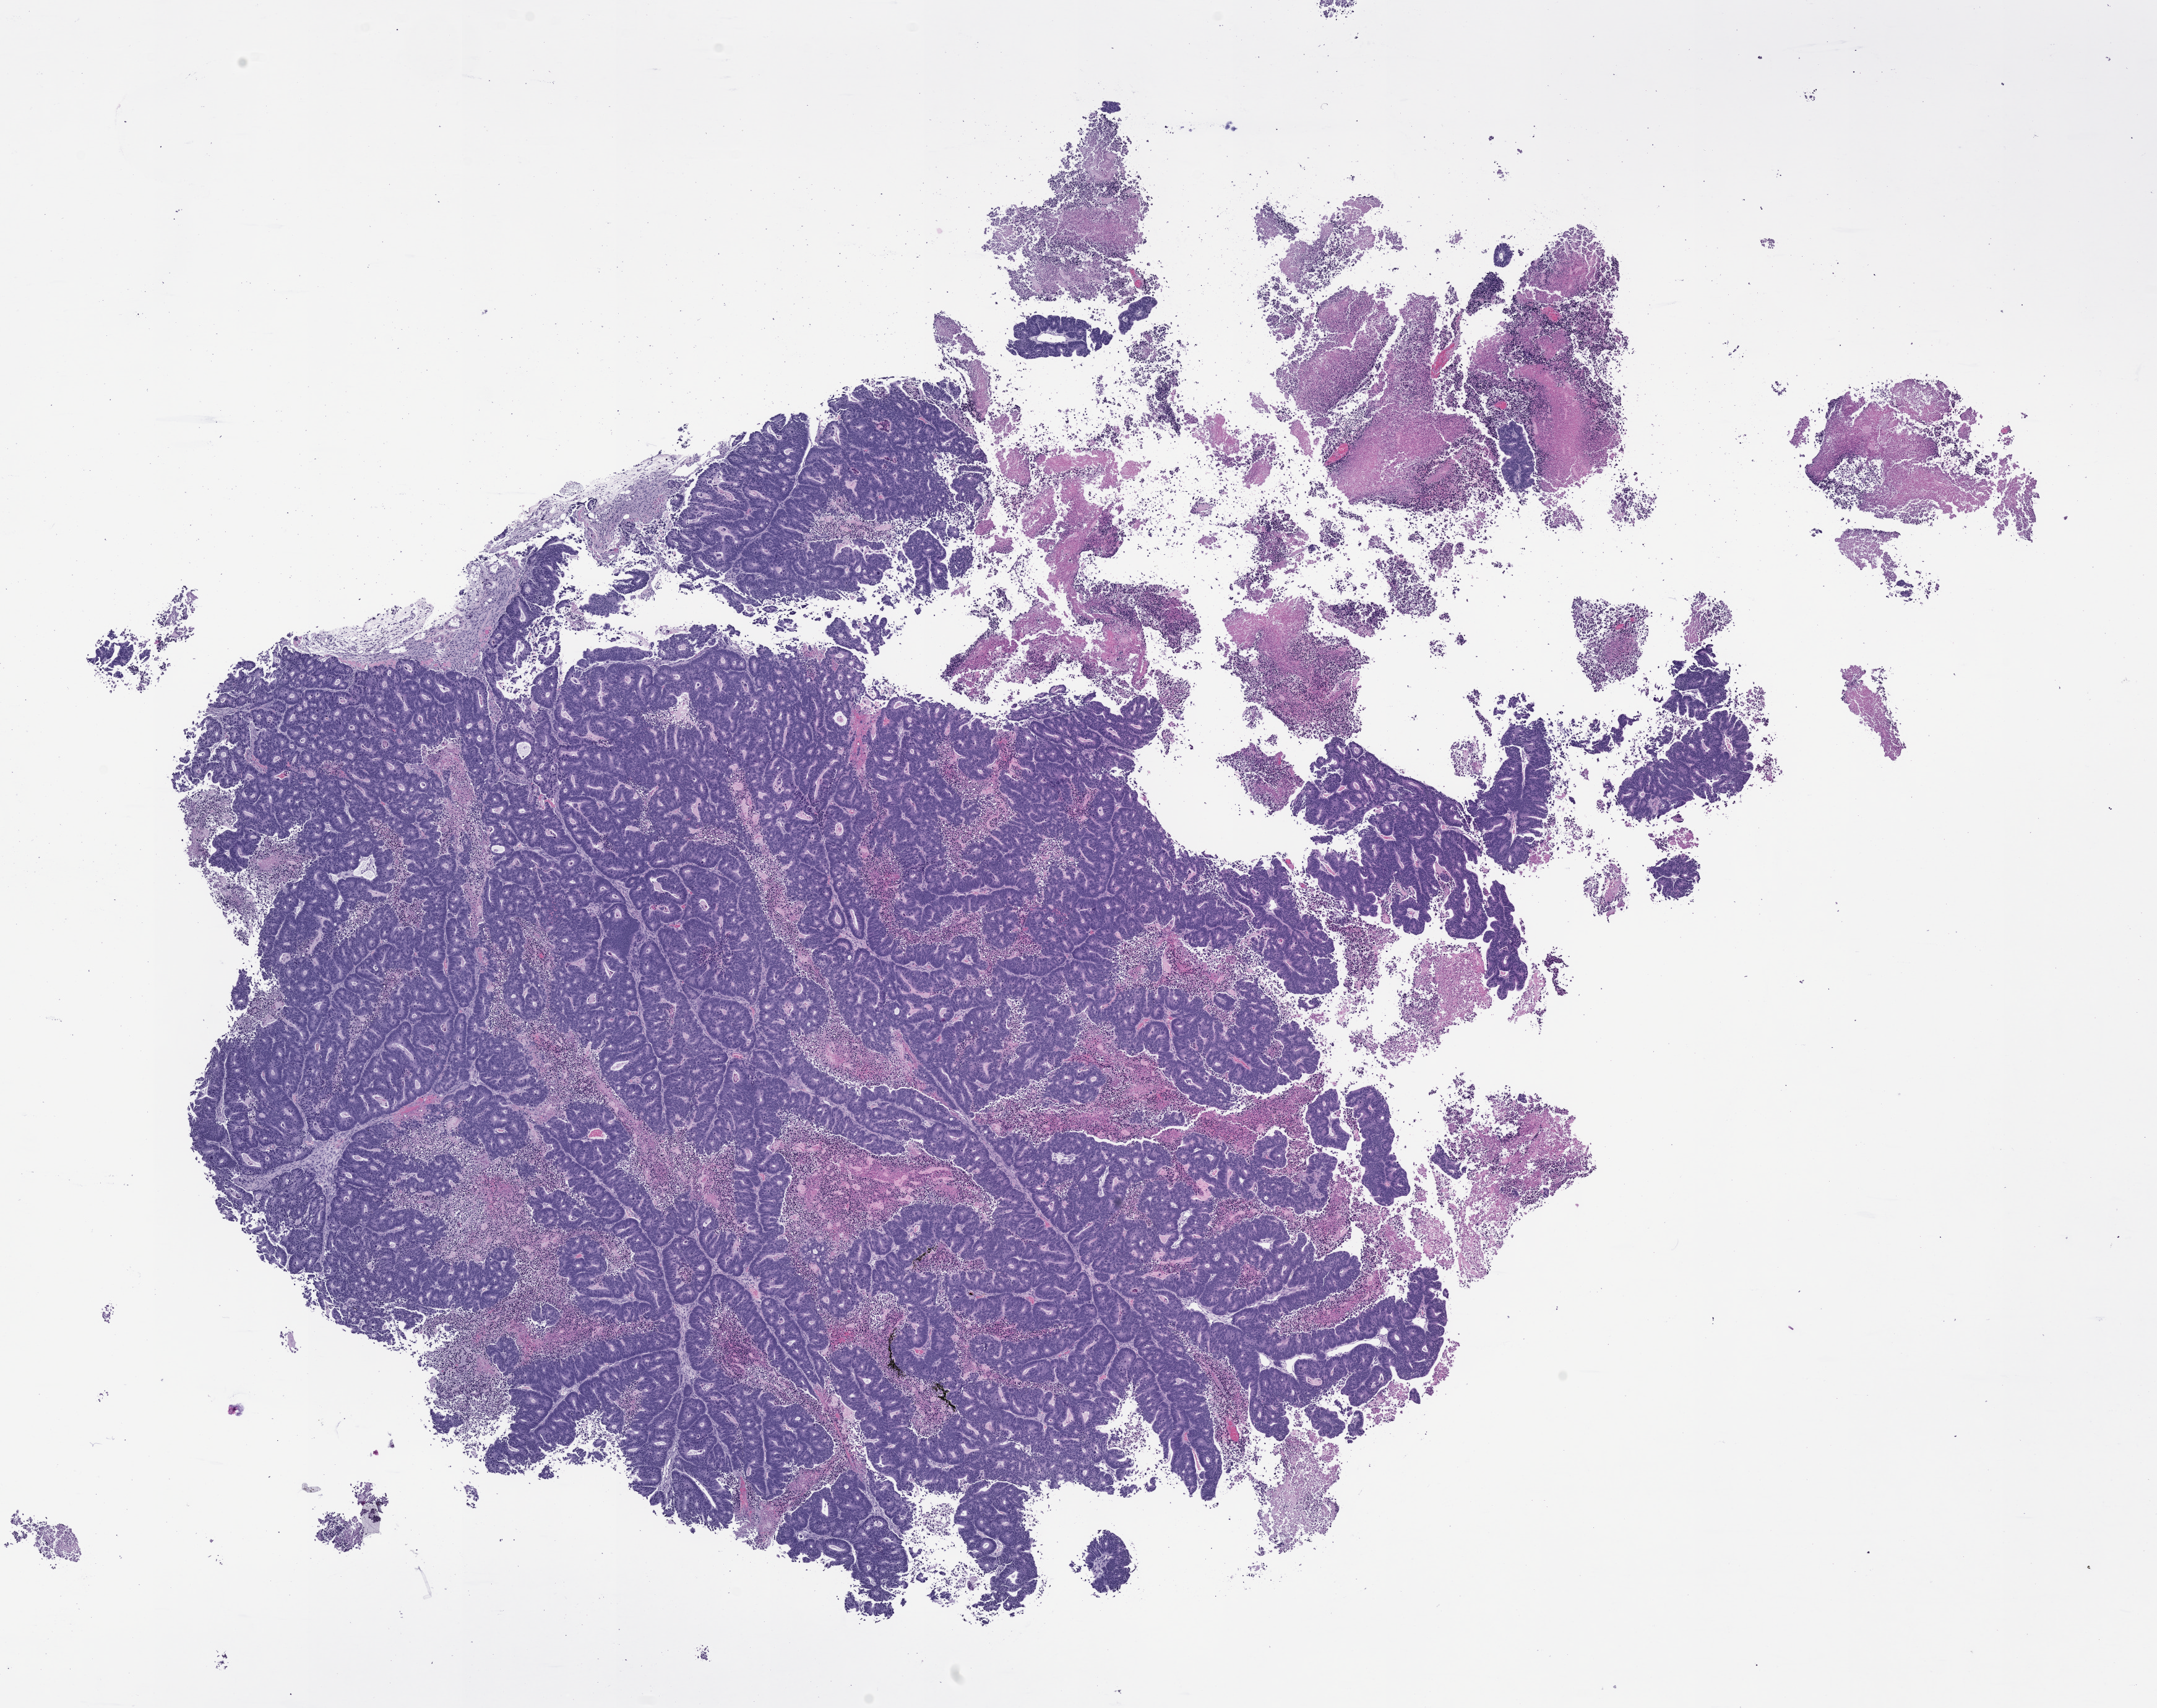
Whole-slide image, H&E: patient-derived xenograft (human tumor grown in a mouse), passage 1 — shown as a low-resolution overview of the whole scanned area (about 14.0 x 11.1 mm); formalin-fixed, paraffin-embedded (FFPE) tissue; tumor site category: rectum.
- originating patient diagnosis: Rectal Adenocarcinoma